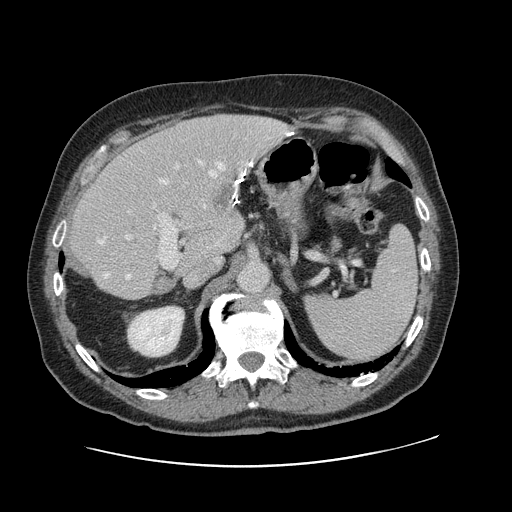
Contrast-enhanced abdominal CT, one axial slice; position 75 of 138 along the scan axis; soft-tissue window (W 400 / L 40 HU); 2.5 mm slice thickness; 512 × 512 image matrix, field of view 402 × 402 mm. Male patient, age 71 years. Case-level facts recorded for this patient, not image findings: diagnosis: colorectal cancer liver metastases, imaged before liver resection; multiple liver metastases: no; largest metastasis: 3.3 cm; disease in both lobes: no.
Annotated regions visible in this slice (manually delineated by an expert):
- hepatic veins: box from (x=98, y=161) to (x=252, y=279) px
- liver: (x=71, y=115)–(x=287, y=300)
- planned liver remnant (the part of the liver to remain after resection): (x=71, y=149)–(x=231, y=300)
- portal vein (with intrahepatic branches): (x=125, y=163)–(x=179, y=268)
- liver metastasis: (x=208, y=183)–(x=233, y=214)